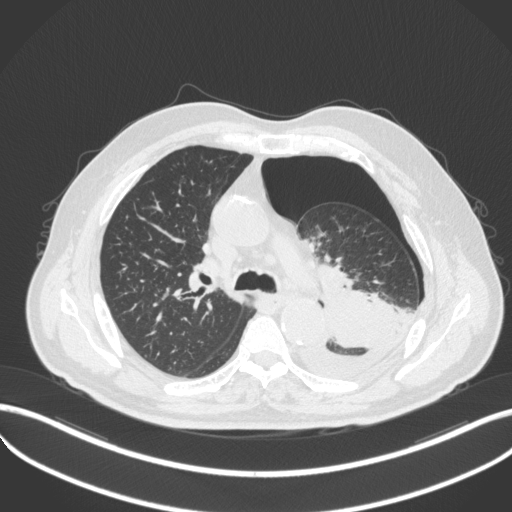
Chest CT, one axial slice; slice 337 of 466 in the series (ordered by position); reconstruction kernel B31f; 120 kVp; lung window (W 1500 / L -600 HU); 1 mm slice thickness; 512 × 512 image matrix, field of view 400 × 400 mm. Male patient, age 76 years. From the clinical record (not read from this slice): clinical TNM (as recorded): T3 N0 M1b.
Structures marked on this image (bounding box drawn by a radiologist):
- lung tumour (recorded histology: adenocarcinoma): bounding box [x1, y1, x2, y2] px = [287, 289, 400, 379]